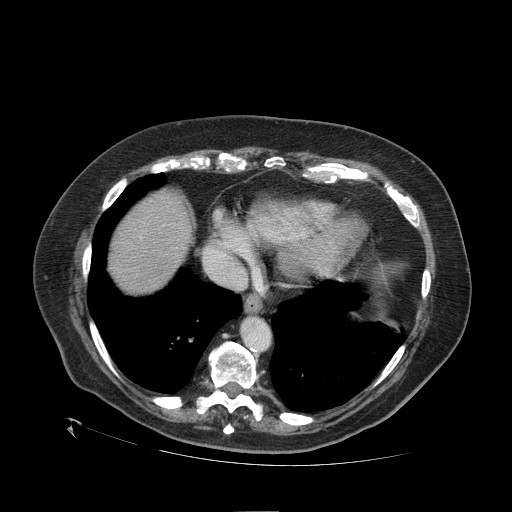
Contrast-enhanced abdominal CT (liver protocol), one axial slice. Slice 96 of 109 in the series (ordered by position). 120 kVp. One of 2 acquisitions stored at this slice position. Soft-tissue window (W 400 / L 40 HU). 2.5 mm slice thickness. 512 × 512 image matrix, field of view 460 × 460 mm. From the clinical record (not read from this slice): diagnosis: hepatocellular carcinoma (patient treated with transarterial chemoembolisation; whether this scan precedes or follows treatment is not stated here); TNM stage (as recorded): Stage-I; Child-Pugh class: A; tumour differentiation: no biopsy; tumour nodularity: uninodular.
Outlined on this slice (semi-automatically segmented with operator editing):
- abdominal aorta: bounding box [x1, y1, x2, y2] px = [242, 318, 270, 350]
- liver parenchyma outside the tumour (the mass and vessels are separate outlines, so this box may not span the whole liver): [108, 190, 192, 292]